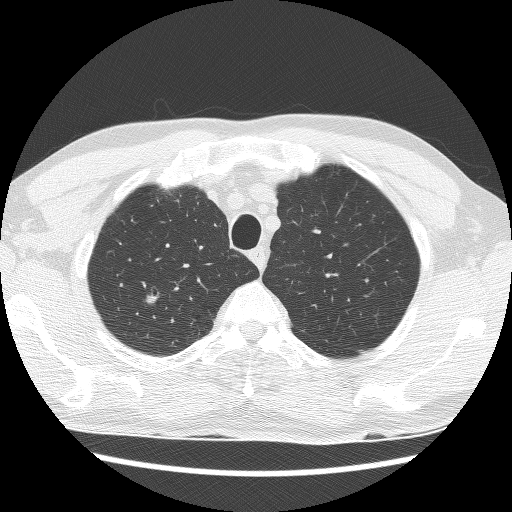
Low-dose screening chest CT, one axial slice. Reconstruction kernel BONE. 120 kVp. Lung window (W 1500 / L -600 HU). 512 × 512 image matrix, field of view 340 × 340 mm.
Outlined on this slice (outlined manually by an expert reader):
- lesion 1 (tumor, upper lobe of right lung): bounding box [x1, y1, x2, y2] px = [145, 293, 159, 307]